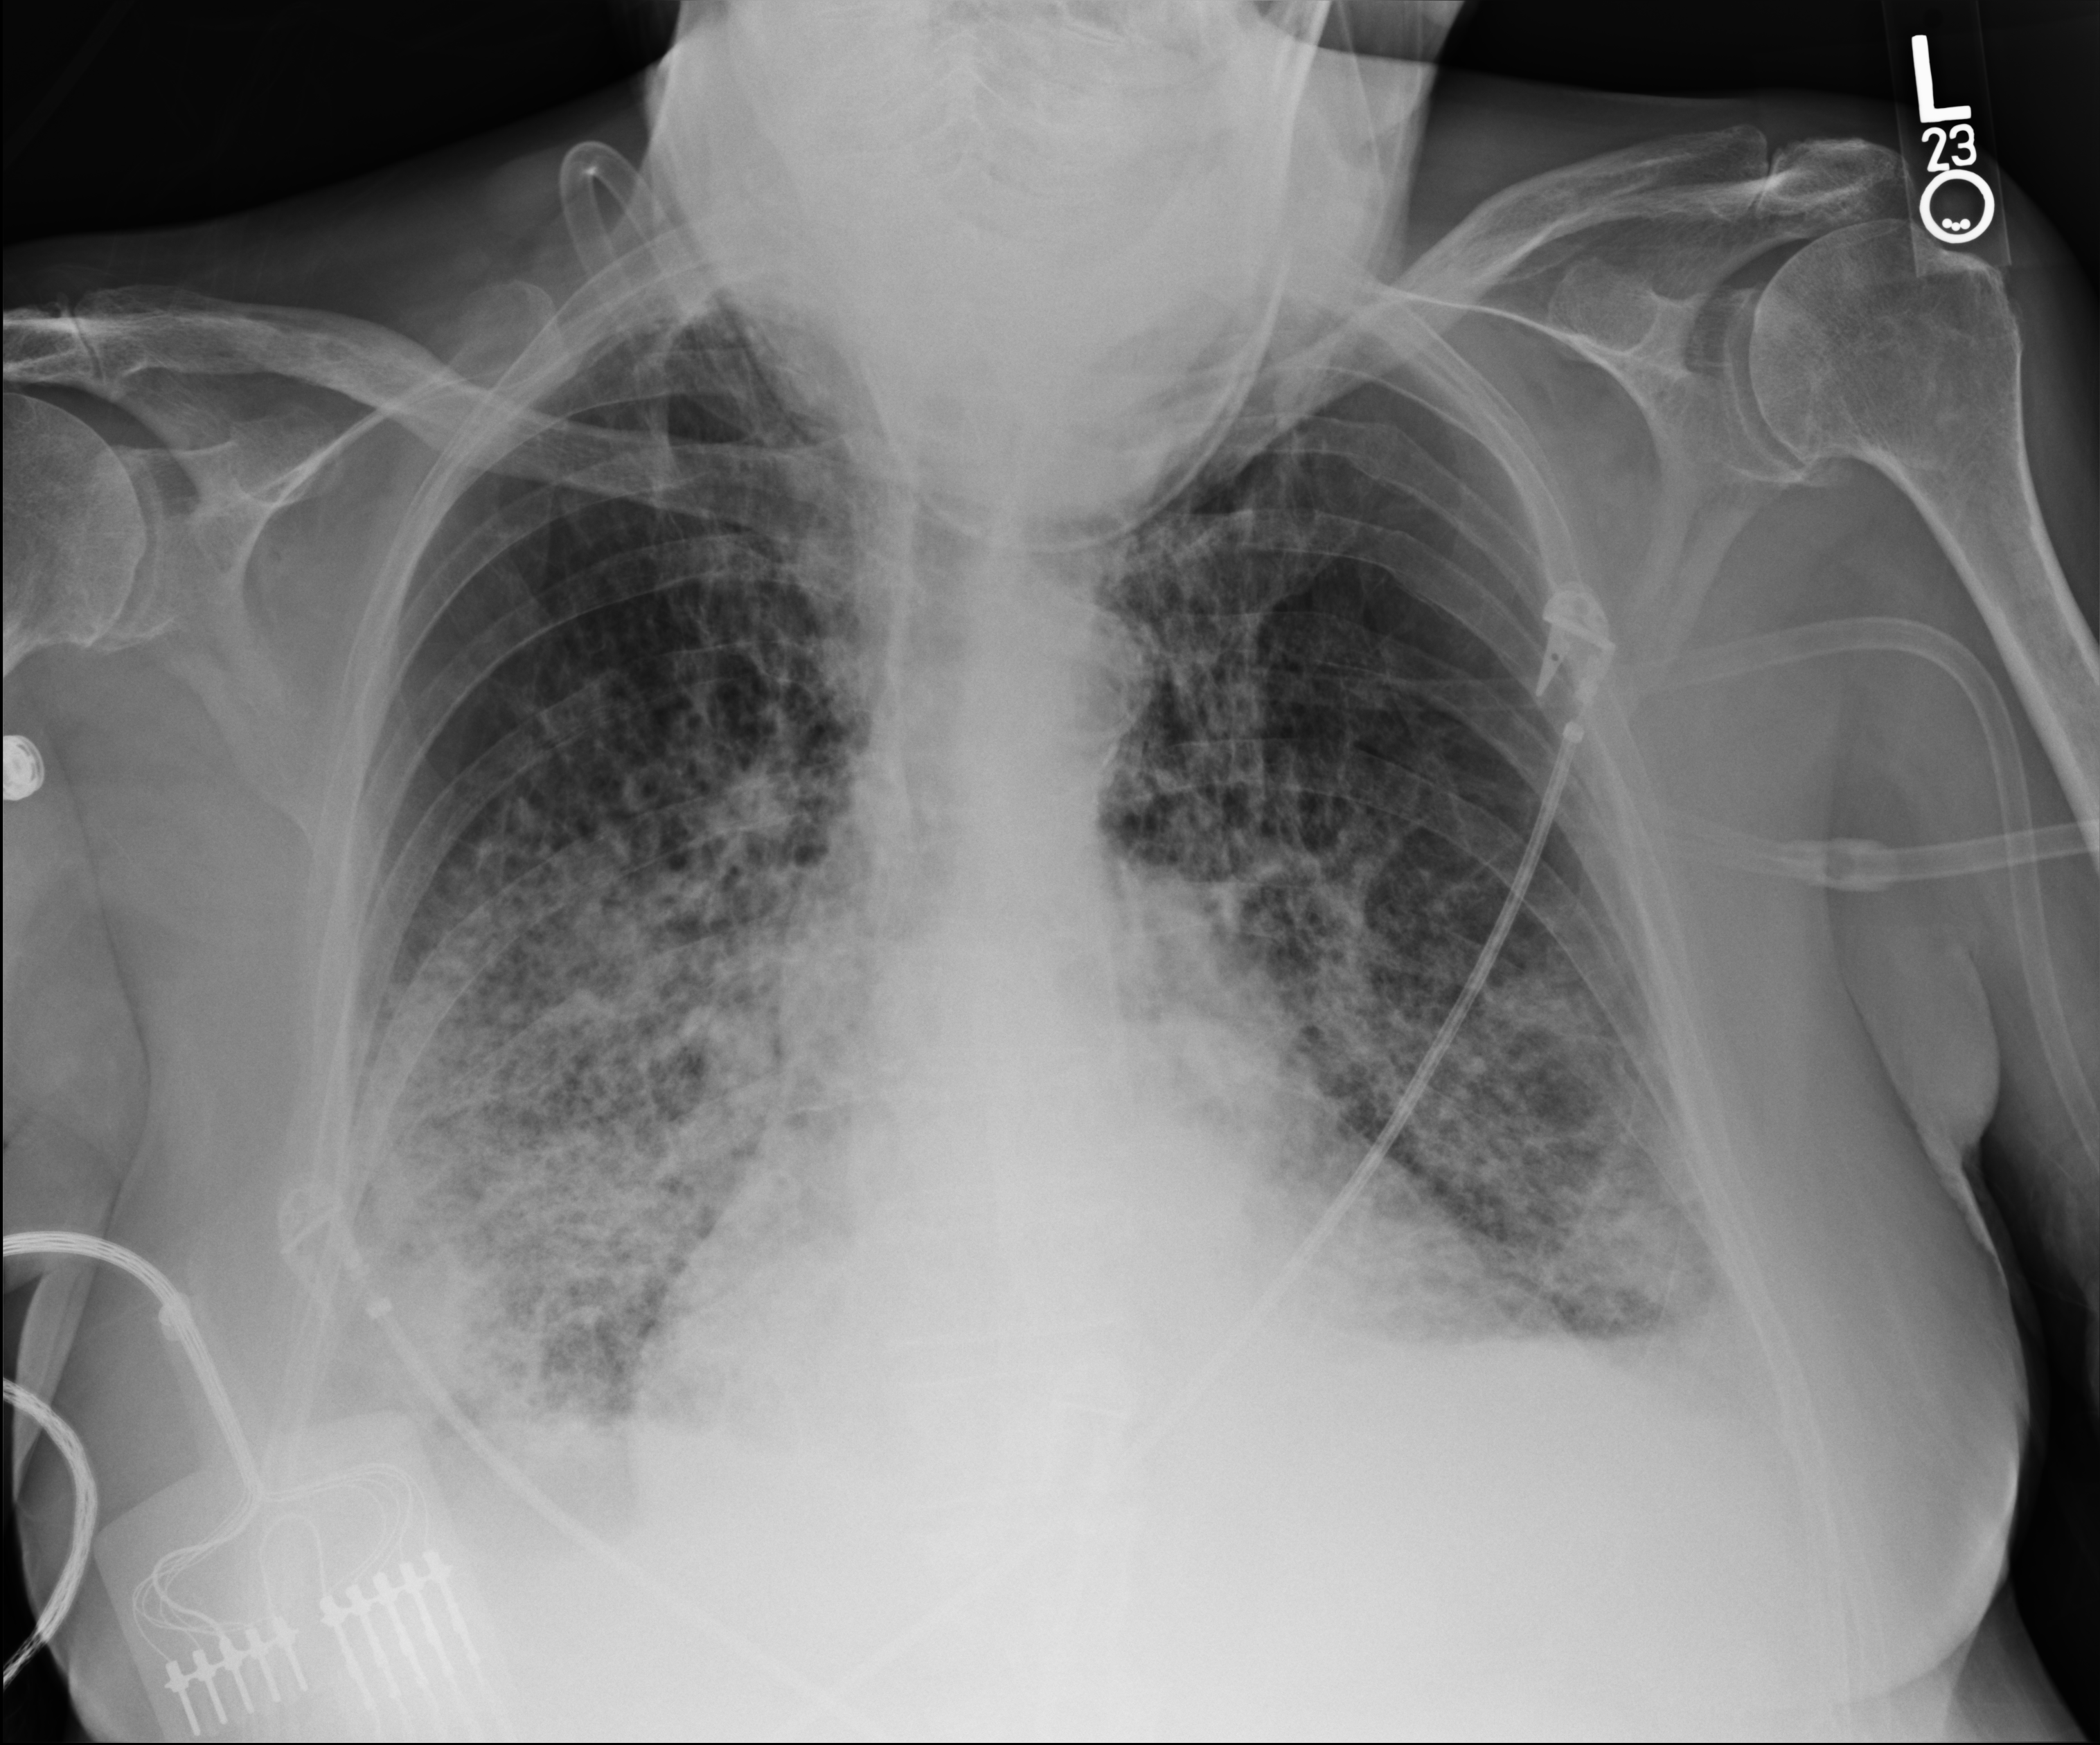
Chest X-ray (portable), anteroposterior (AP) projection. Male patient hospitalised with COVID-19, age 75–90 years.
Hospital-stay facts (about this admission, not read from this image; timing relative to this image not recorded):
- smoking status (admission record): former